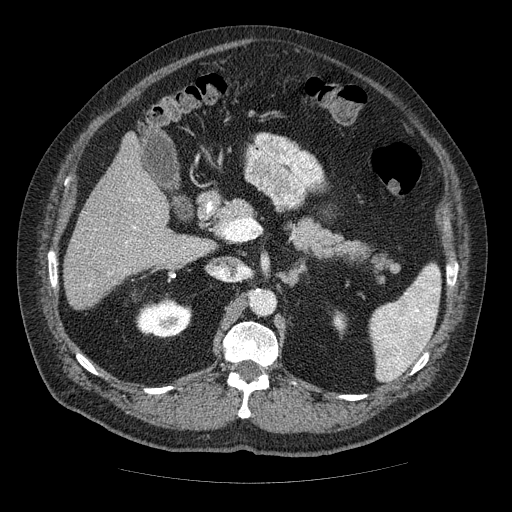
Contrast-enhanced abdominal CT (liver protocol), one axial slice; position 24 of 85 along the scan axis; reconstruction kernel STANDARD; 120 kVp; soft-tissue window (W 400 / L 40 HU); 512 × 512 image matrix. From the clinical record (not read from this slice): diagnosis: hepatocellular carcinoma (patient treated with transarterial chemoembolisation; whether this scan precedes or follows treatment is not stated here); TNM stage (as recorded): Stage-IIIA; Child-Pugh class: A; tumour nodularity: multinodular; tumour size: 7 cm.
Annotated regions visible in this slice (semi-automatically segmented with operator editing):
- liver parenchyma outside the tumour (the mass and vessels are separate outlines, so this box may not span the whole liver): bounding box <64,132,211,310> (left, top, right, bottom; pixels)
- liver vessels: <89,217,158,286>